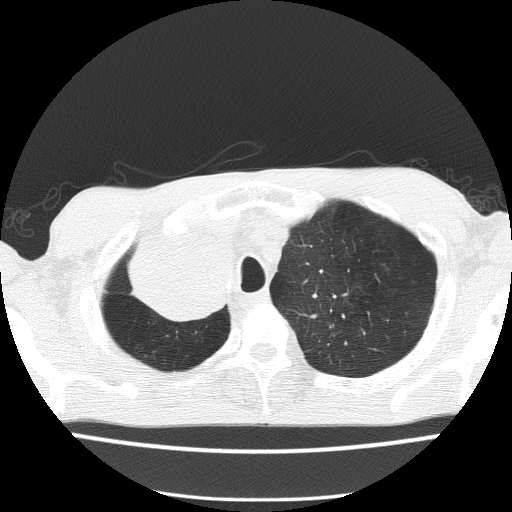
Low-dose screening chest CT, one axial slice. Position 123 of 150 along the scan axis. Reconstruction kernel FC51. Lung window (W 1500 / L -600 HU). 2 mm slice thickness. 512 × 512 image matrix.
Structures marked on this image (expert manual segmentation):
- lesion 1 (tumor, hilum of right lung): bounding box [x1, y1, x2, y2] px = [131, 228, 229, 320]